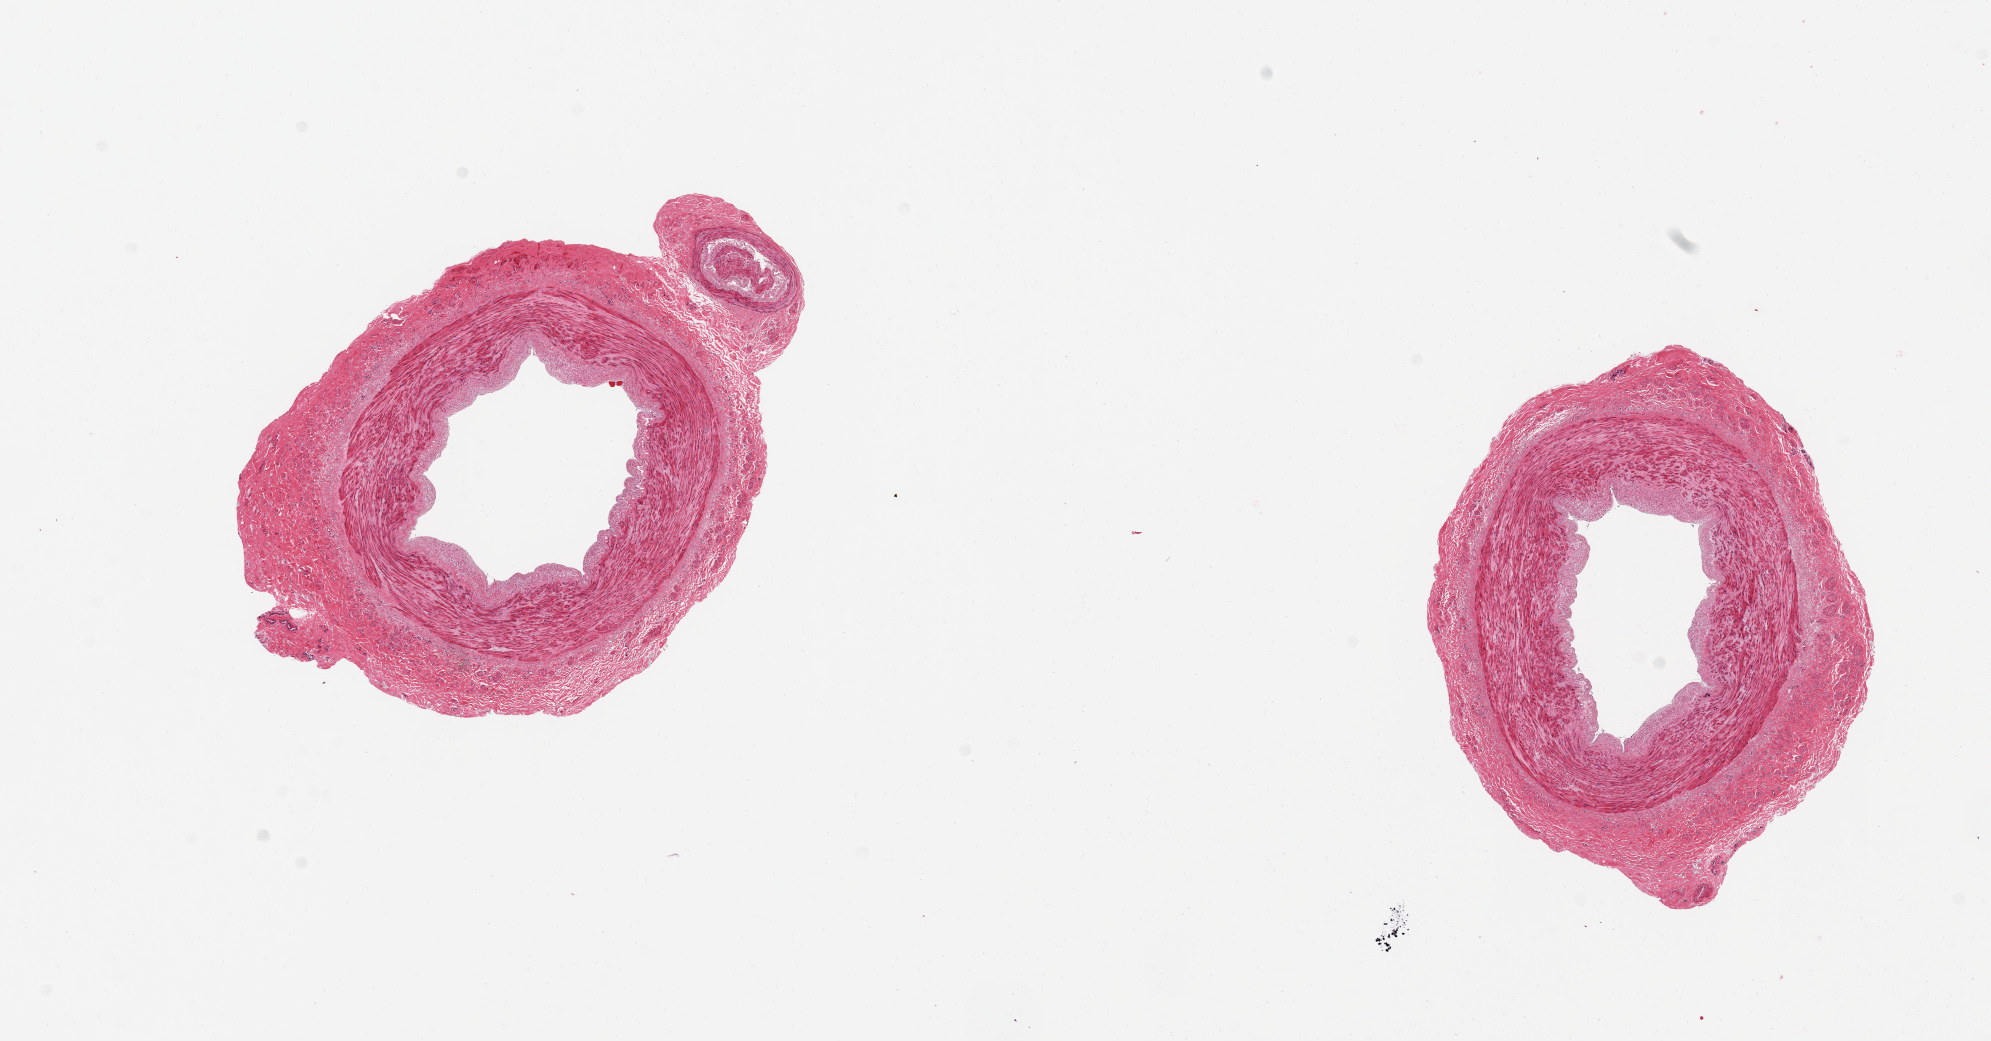
Whole-slide image, haematoxylin and eosin stain, brightfield, whole scanned area (about 15.8 x 8.2 mm, from a 20x scan) shown as a low-resolution overview. PAXgene-fixed, paraffin-embedded tissue. Target tissue: tibial artery. Donor tissue sample.
Review note (as recorded): 2 pieces; well trimmed, no lesions.